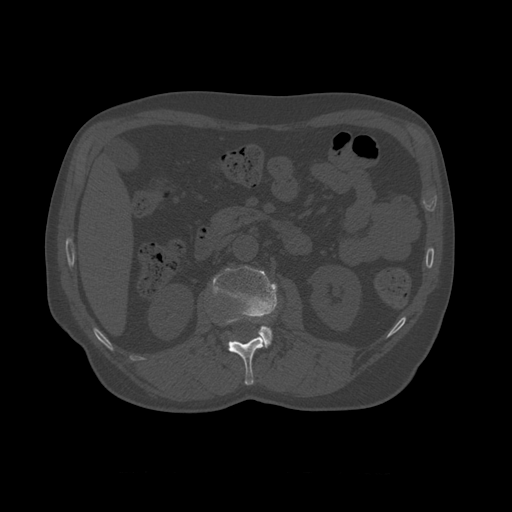
CT including the spine, one axial slice. Slice 345 of 450 in the series (ordered by position). Reconstruction kernel STANDARD. 120 kVp. Bone window (W 1800 / L 400 HU). 1.25 mm slice thickness. 512 × 512 image matrix, field of view 405 × 405 mm. Patient age 75 years. Case-level facts recorded for this patient, not image findings: primary cancer: prostate.
Structures marked on this image (semi-automatic segmentation, software-assisted and operator-edited):
- L1 vertebra: box from (x=213, y=318) to (x=265, y=386) px
- L2 vertebra: (x=212, y=266)–(x=279, y=348)